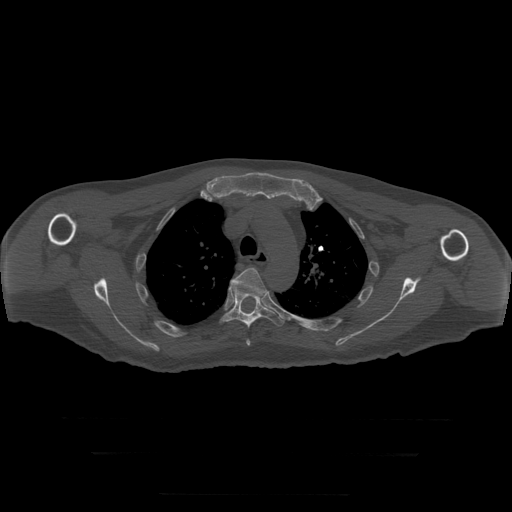
CT including the spine, one axial slice. Position 231 of 397 along the scan axis. 120 kVp. Bone window (W 1800 / L 400 HU). 1.25 mm slice thickness. 512 × 512 image matrix. Patient age 73 years. From the clinical record (not read from this slice): primary cancer: prostate.
Structures marked on this image (semi-automatically segmented with operator editing):
- T4 vertebra: bounding box [x1, y1, x2, y2] px = [230, 268, 267, 346]
- T5 vertebra: [219, 284, 285, 328]